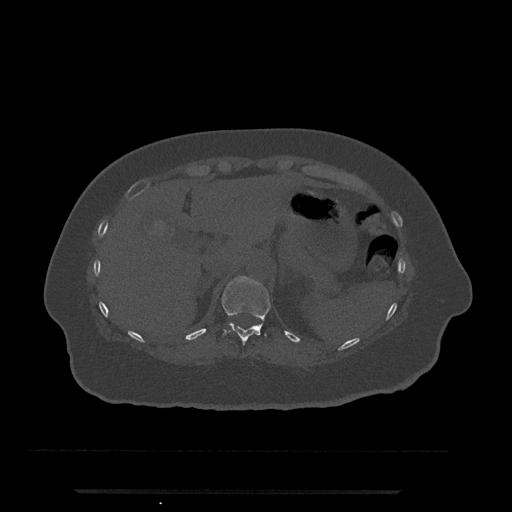
CT including the spine, one axial slice. Slice 224 of 797 in the series (ordered by position). Reconstruction kernel Br40s/3. 120 kVp. Bone window (W 1800 / L 400 HU). 512 × 512 image matrix, field of view 440 × 440 mm. Patient: female, 51 years. Case-level facts recorded for this patient, not image findings: primary cancer: neuro.
Outlined on this slice (semi-automatically segmented with operator editing):
- T11 vertebra: bounding box [x1, y1, x2, y2] px = [222, 276, 271, 345]